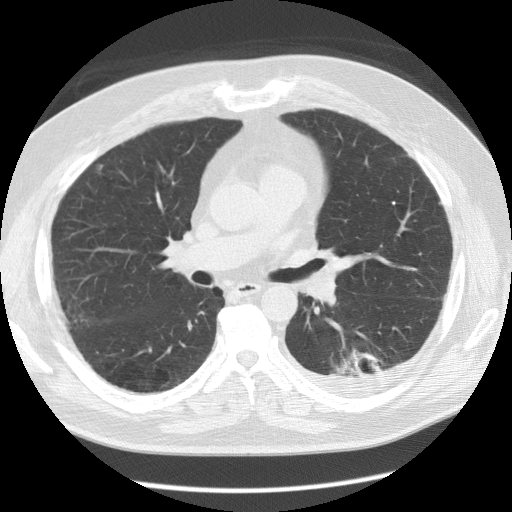
Chest CT (low-dose screening protocol), one axial image. Baseline screening round. Lung window (W 1500 / L -600 HU). 120 kVp. Slice 54 of 126 in the series. Male participant, aged 56 years at enrolment. Former smoker at enrolment.
Lesion marked by an expert reader, bounding box (x1, y1, x2, y2) in pixels: (323, 338, 394, 391). The screening reader recorded 4 non-calcified nodules or masses ≥4 mm on this exam; which of them this box marks is not recorded. Official screen result: positive, change unspecified: nodule(s) >= 4 mm or enlarging nodule(s), mass(es), or other non-specific abnormalities suspicious for lung cancer. Participant outcome: lung cancer diagnosed 173 days after this screen — non-small cell carcinoma, left lower lobe, stage IV (AJCC 6th edition), 50 mm at pathology.